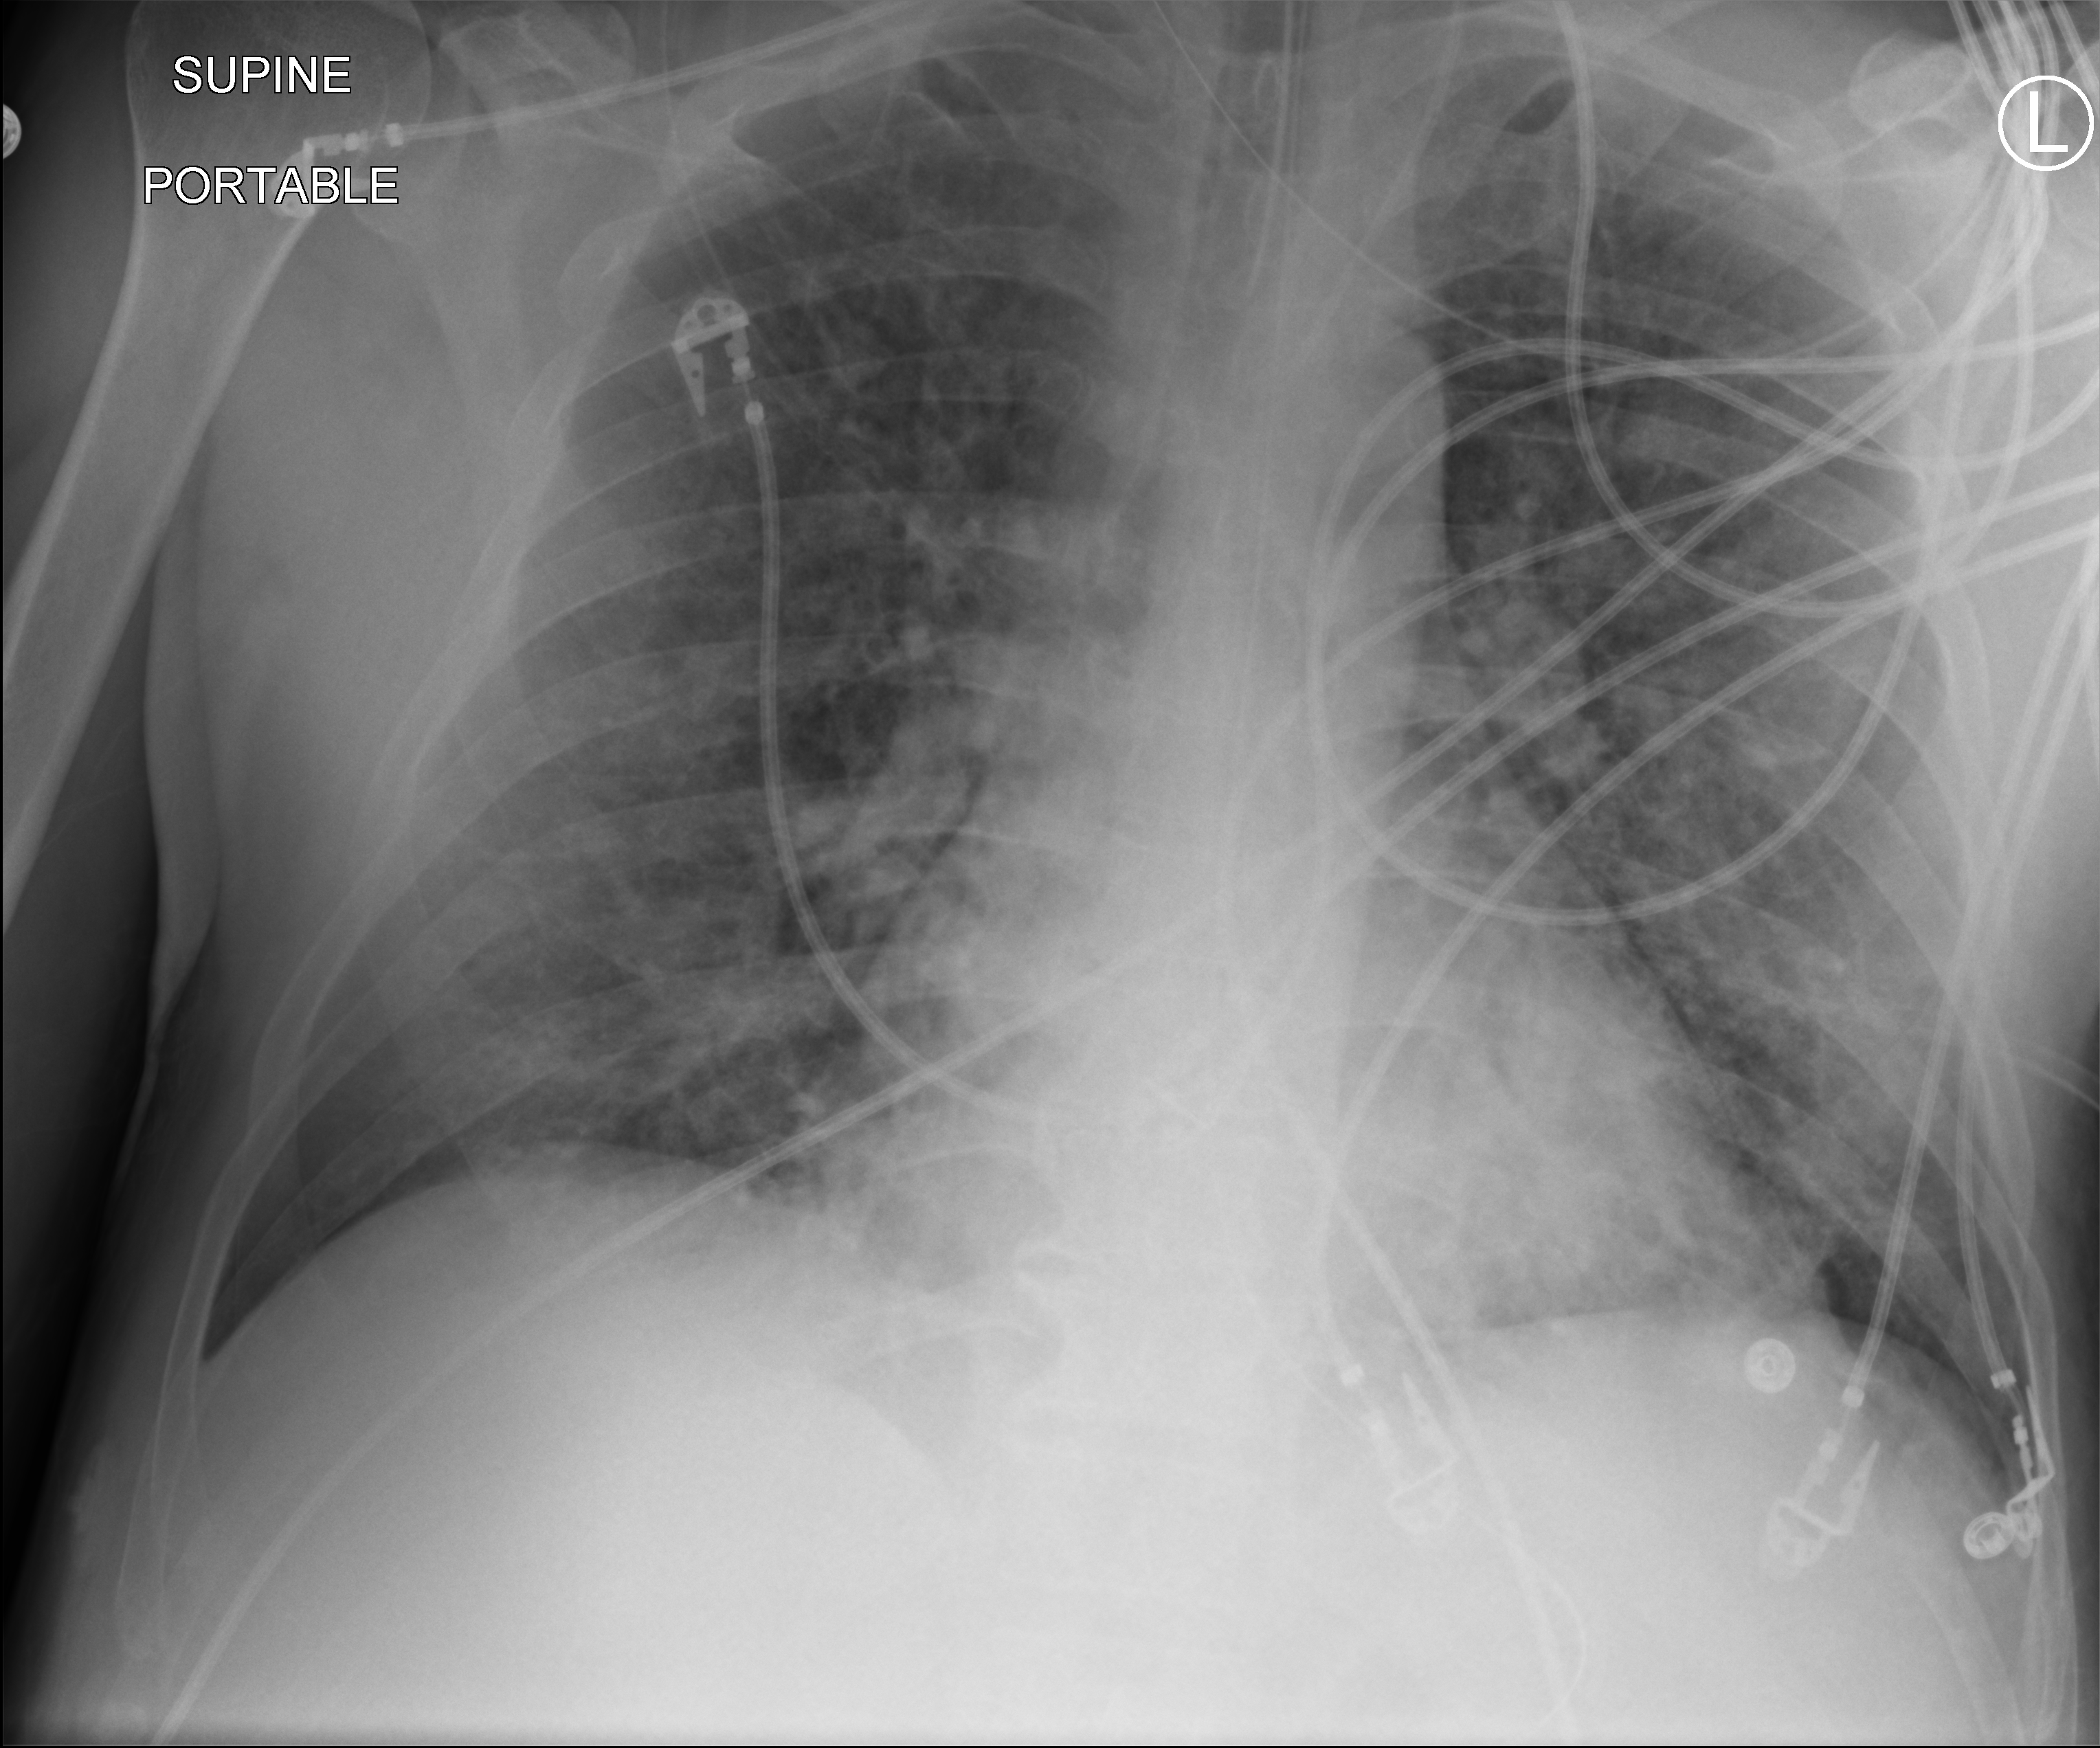
Bedside chest radiograph (computed radiography), anteroposterior (AP) projection. Male patient hospitalised with COVID-19, age 18–59 years.
From the hospital-stay record, not from the radiograph (when in the stay this image was taken is not recorded):
- admitted to intensive care during this hospital stay: no
- mechanically ventilated during this hospital stay: yes
- length of hospital stay: 19 days